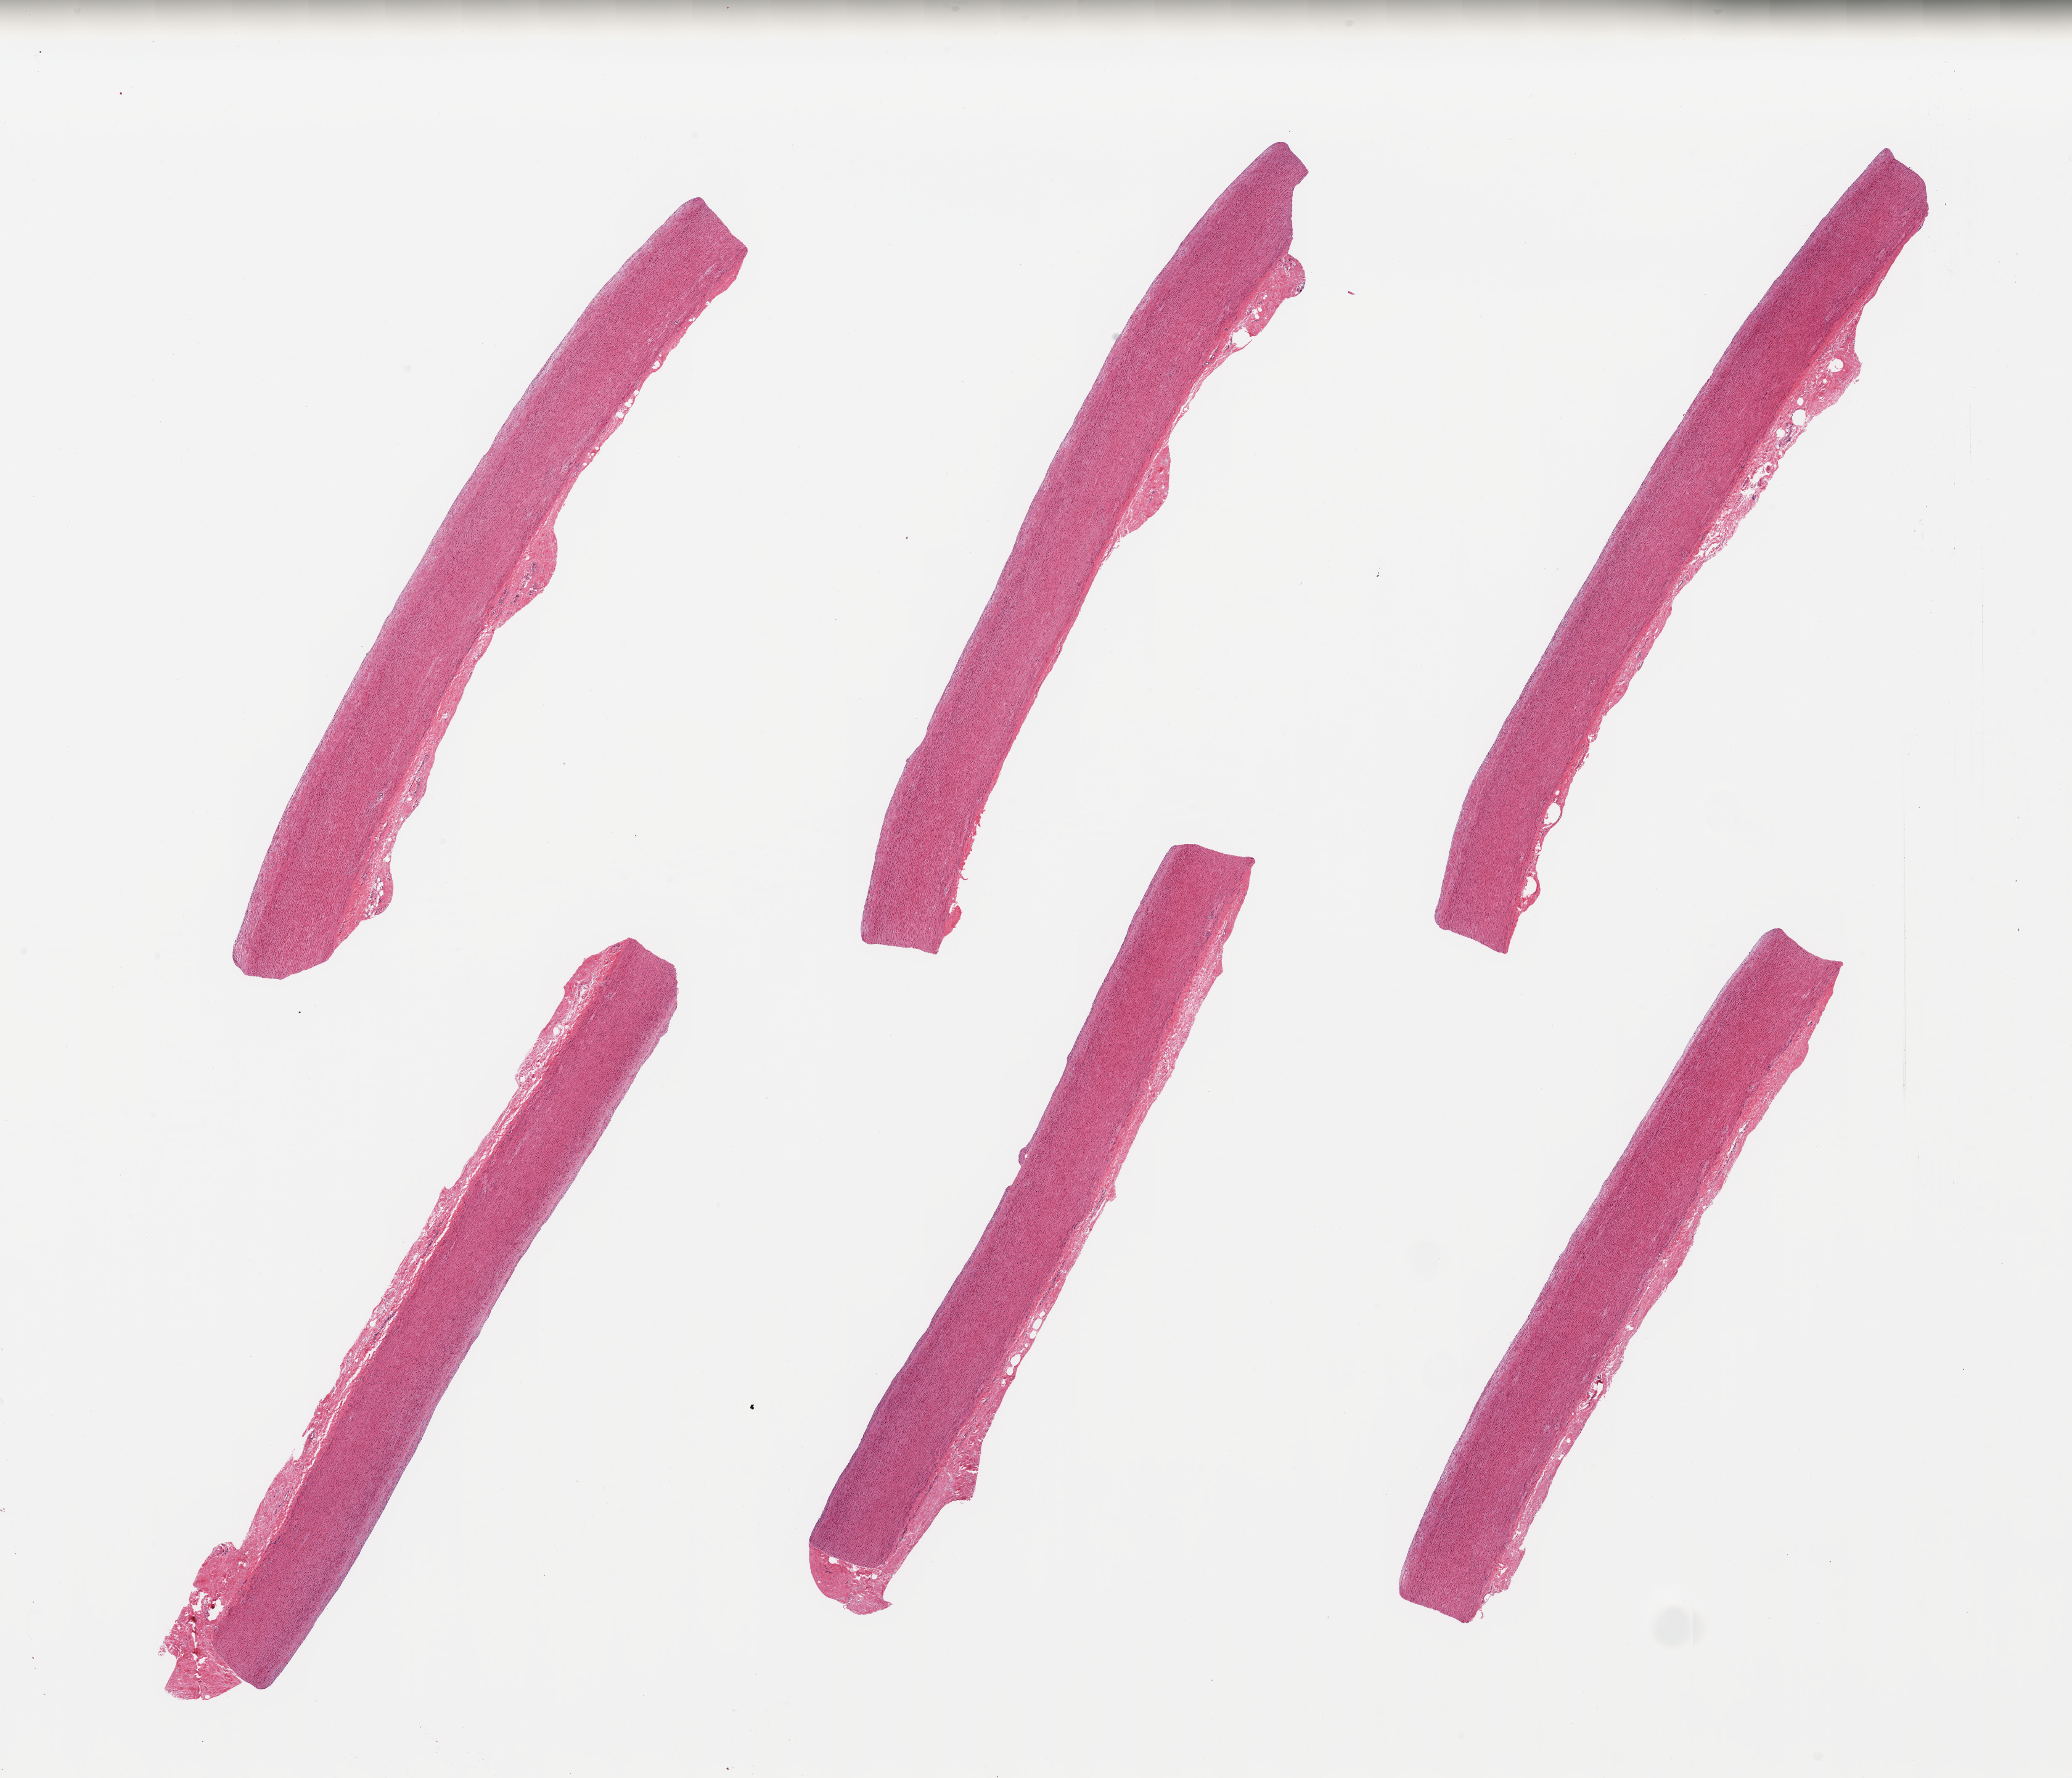
Digitized haematoxylin and eosin-stained section, brightfield, a low-resolution overview of the entire scanned area, about 26.6 x 22.8 mm. PAXgene-fixed paraffin-embedded (PFPE) section. Section of aorta (target tissue). Tissue donor sample.
Review note (as recorded): 6 pieces, trace atherosis.